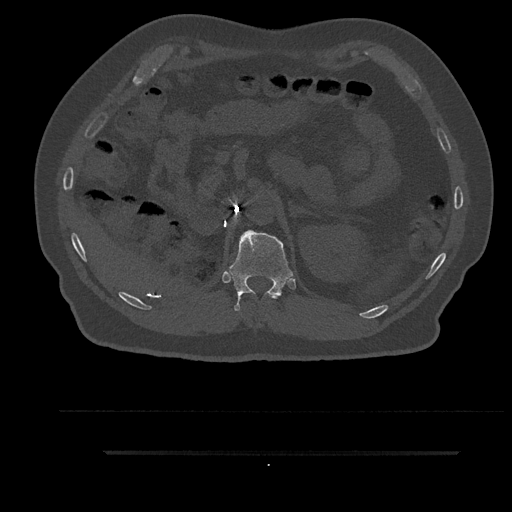
CT including the spine, one axial slice; slice 257 of 797 in the series (ordered by position); reconstruction kernel Br40s/3; bone window (W 1800 / L 400 HU); 0.5 mm slice thickness; 512 × 512 image matrix. Patient: male, 63 years. Case-level facts recorded for this patient, not image findings: primary cancer: renal; vertebrae with lytic lesions (as recorded): T8.
Annotated regions visible in this slice (semi-automatic segmentation, software-assisted and operator-edited):
- T11 vertebra: bounding box (x1, y1, x2, y2) in pixels: (269, 295, 278, 299)
- T12 vertebra: (227, 230, 294, 311)